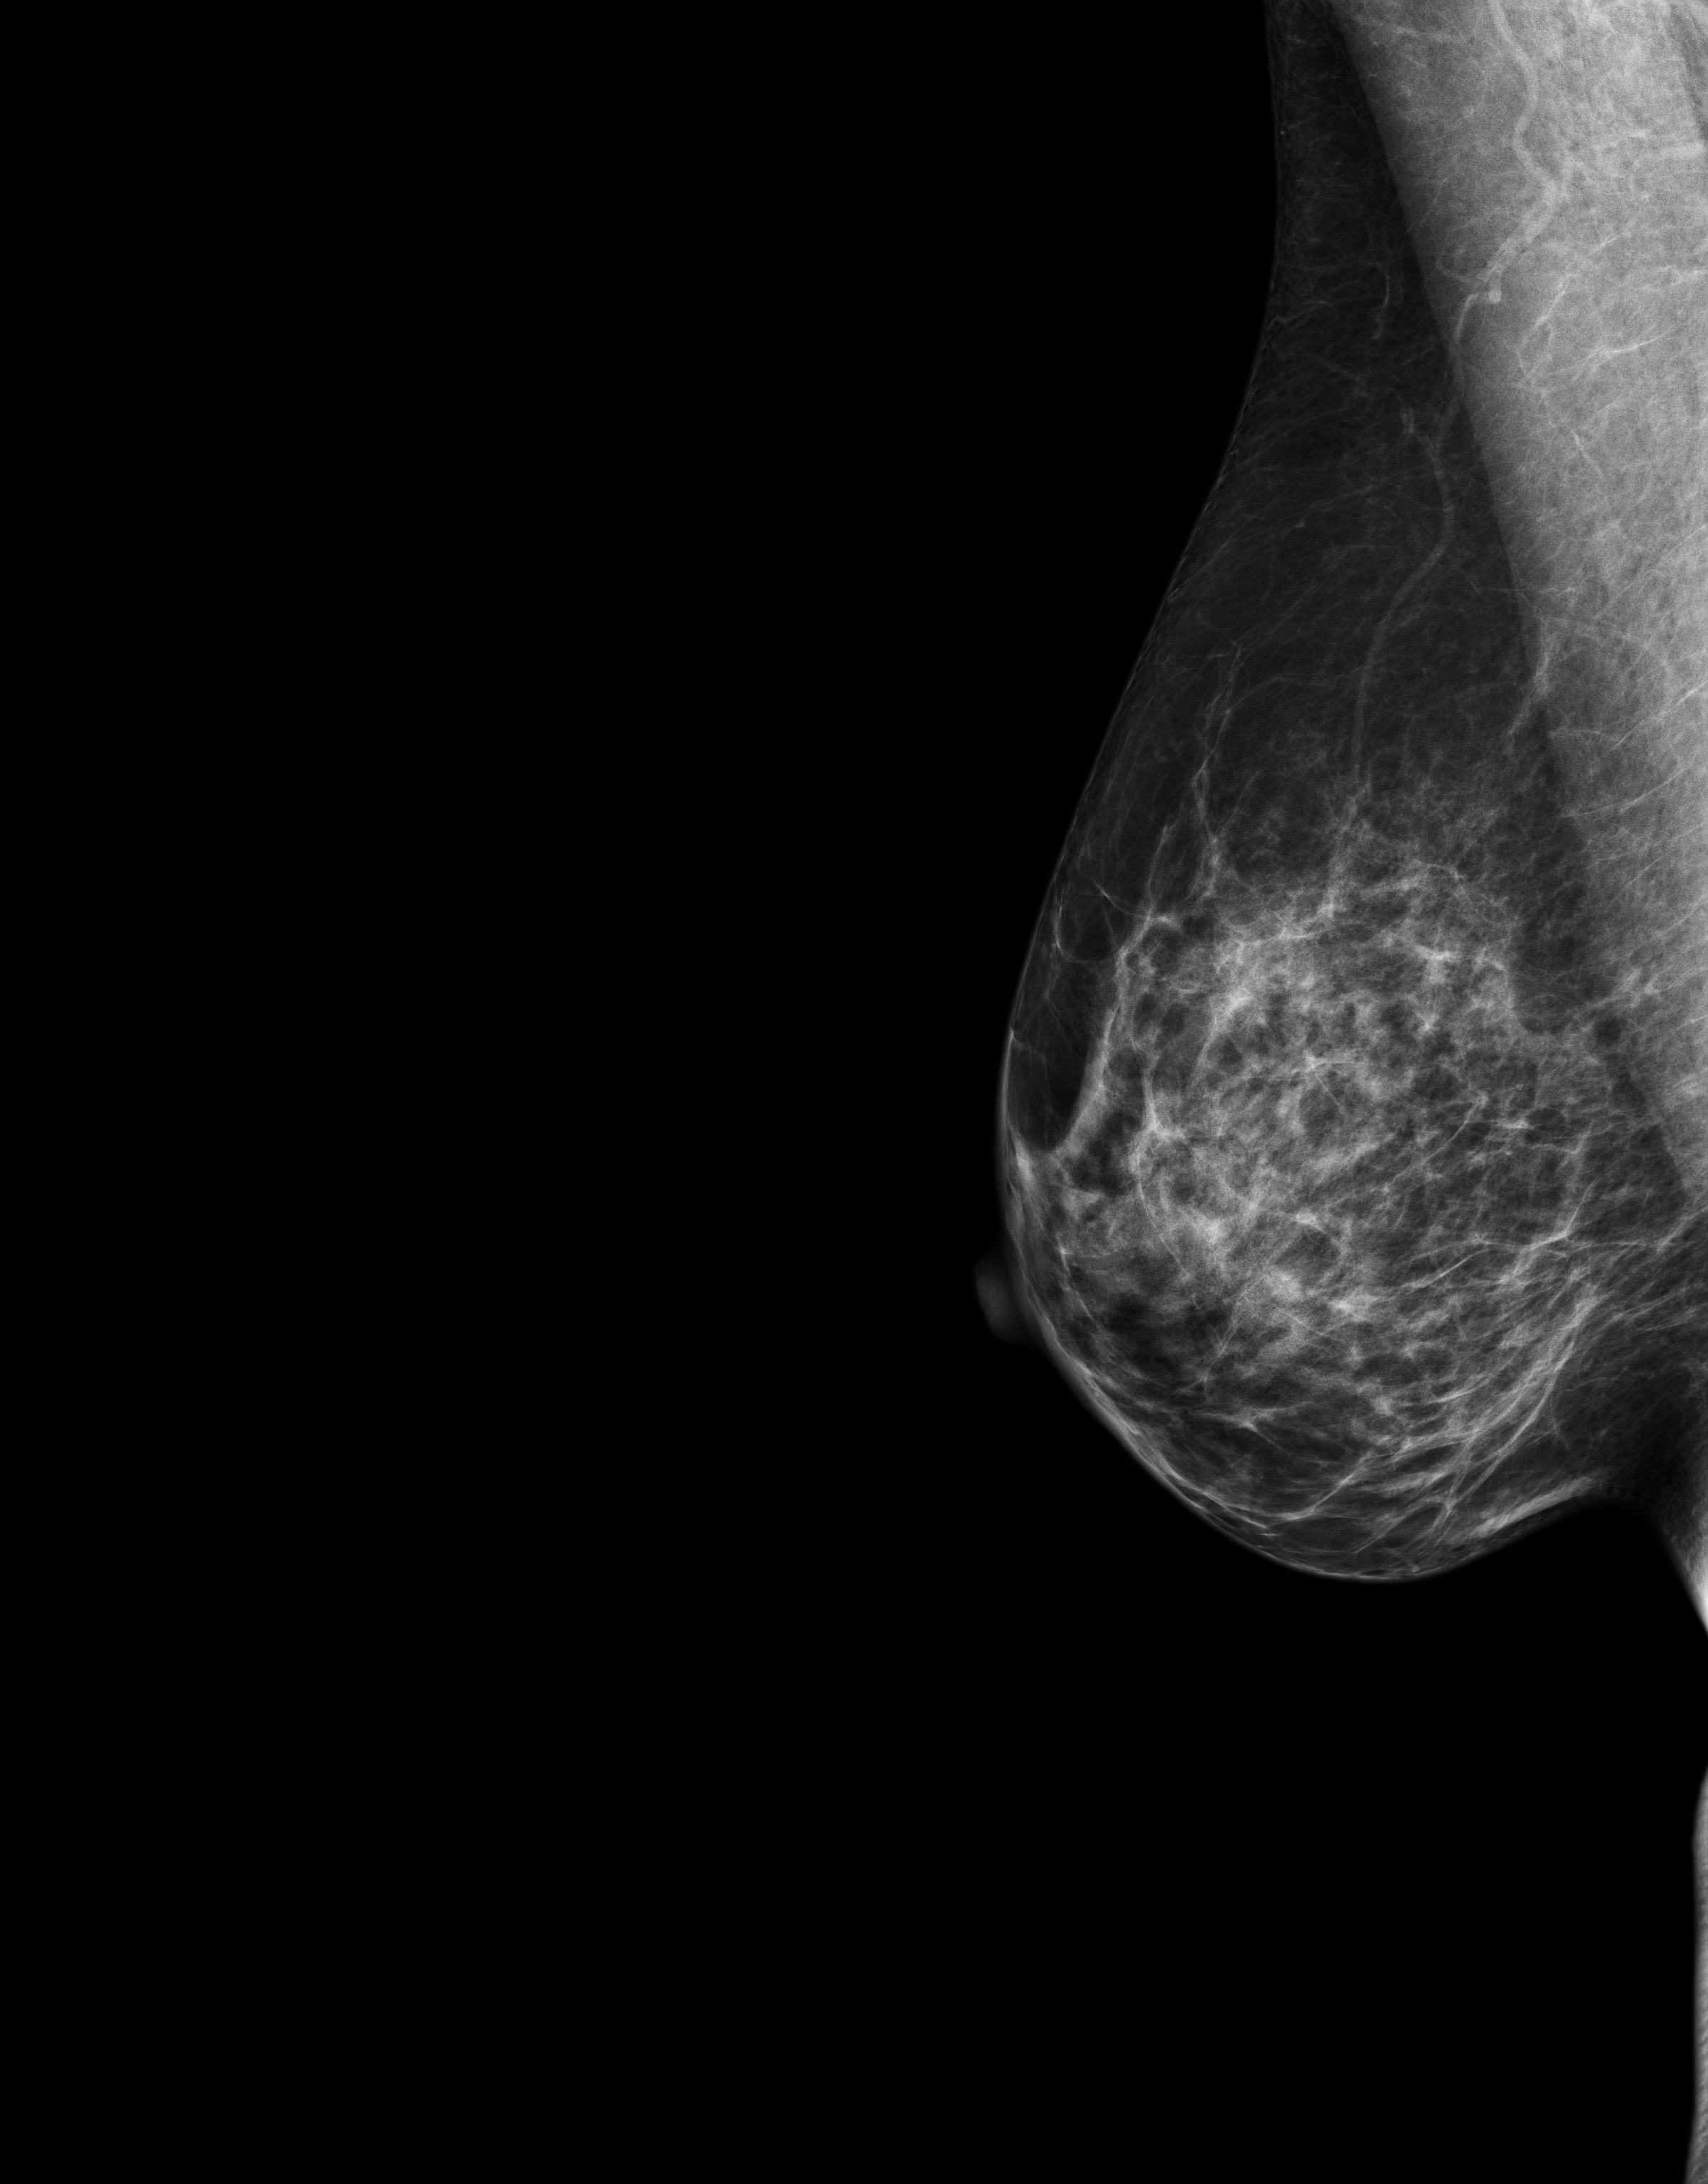
Digital mammogram (FFDM); right breast; mediolateral oblique (MLO) view; annual screening mammography examination; compressed breast thickness 57 mm. Female patient, age 56 years.
Breast density at the screening exam (both breasts): heterogeneously dense (BI-RADS density category c). Final BI-RADS category for the screening round (tomosynthesis exam, both breasts): category 1. Recall: no recall after this screen.